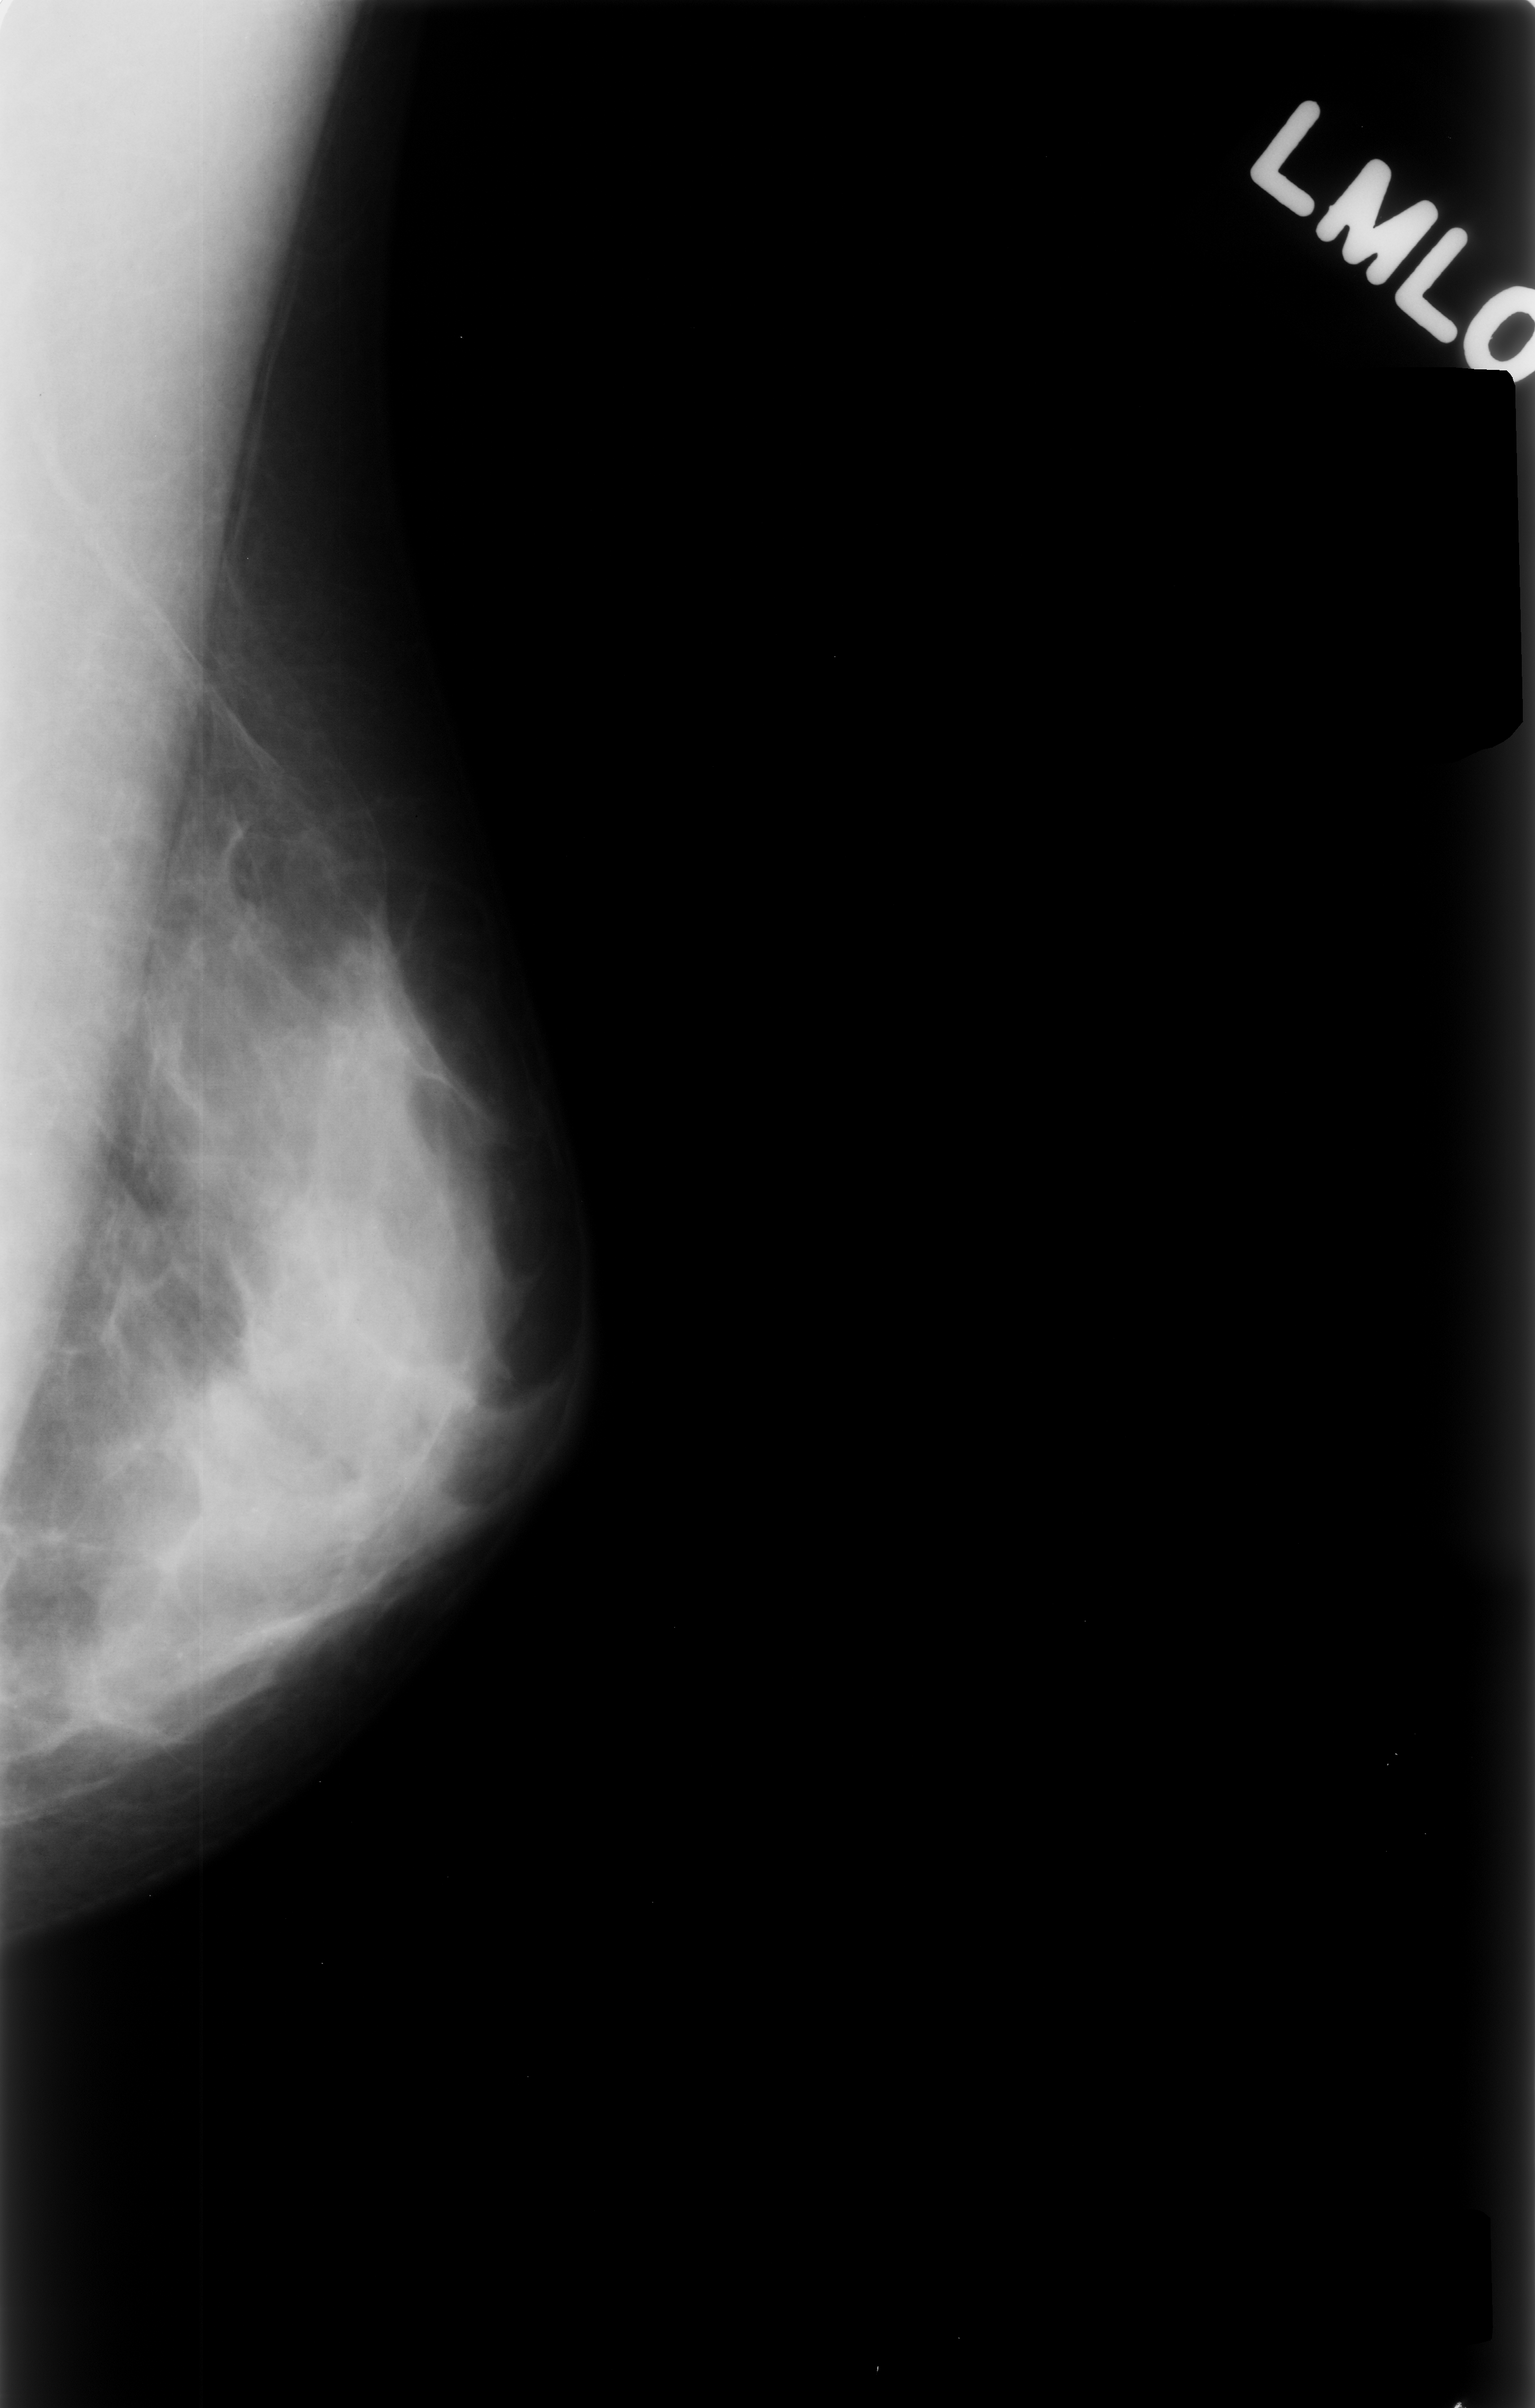
Mammogram (digitized film), left breast, MLO view, breast composition: extremely dense (BI-RADS density category 4 of 4).
- Calcifications, morphology punctate, distribution clustered; BI-RADS assessment category 4; subtlety rating 3 on a 1 (subtle) to 5 (obvious) scale; pathology (as recorded): benign.